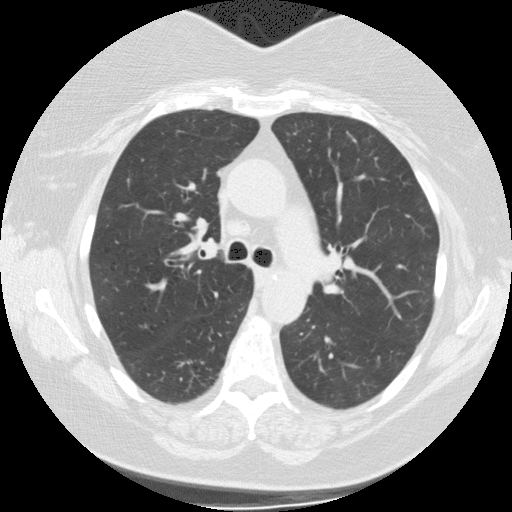
Low-dose screening chest CT, axial slice; first (baseline) screen; lung window (W 1500 / L -600 HU); standard (soft-tissue) reconstruction kernel (STANDARD); slice 44 of 130 in the series. Female, age 62 years at enrolment. Current smoker at enrolment.
• Lesion marked by an expert reader, bounding box <196,152,239,194> (left, top, right, bottom; pixels).
• The screening reader recorded 3 non-calcified nodules or masses ≥4 mm on this exam (right lower lobe, right lower lobe, right lower lobe); which of them this box marks is not recorded.
• Lung cancer was diagnosed 929 days after this screen (after the third annual screen): adenocarcinoma, NOS, right upper lobe, poorly differentiated (G3), stage IB (AJCC 6th edition), 12 mm at pathology.